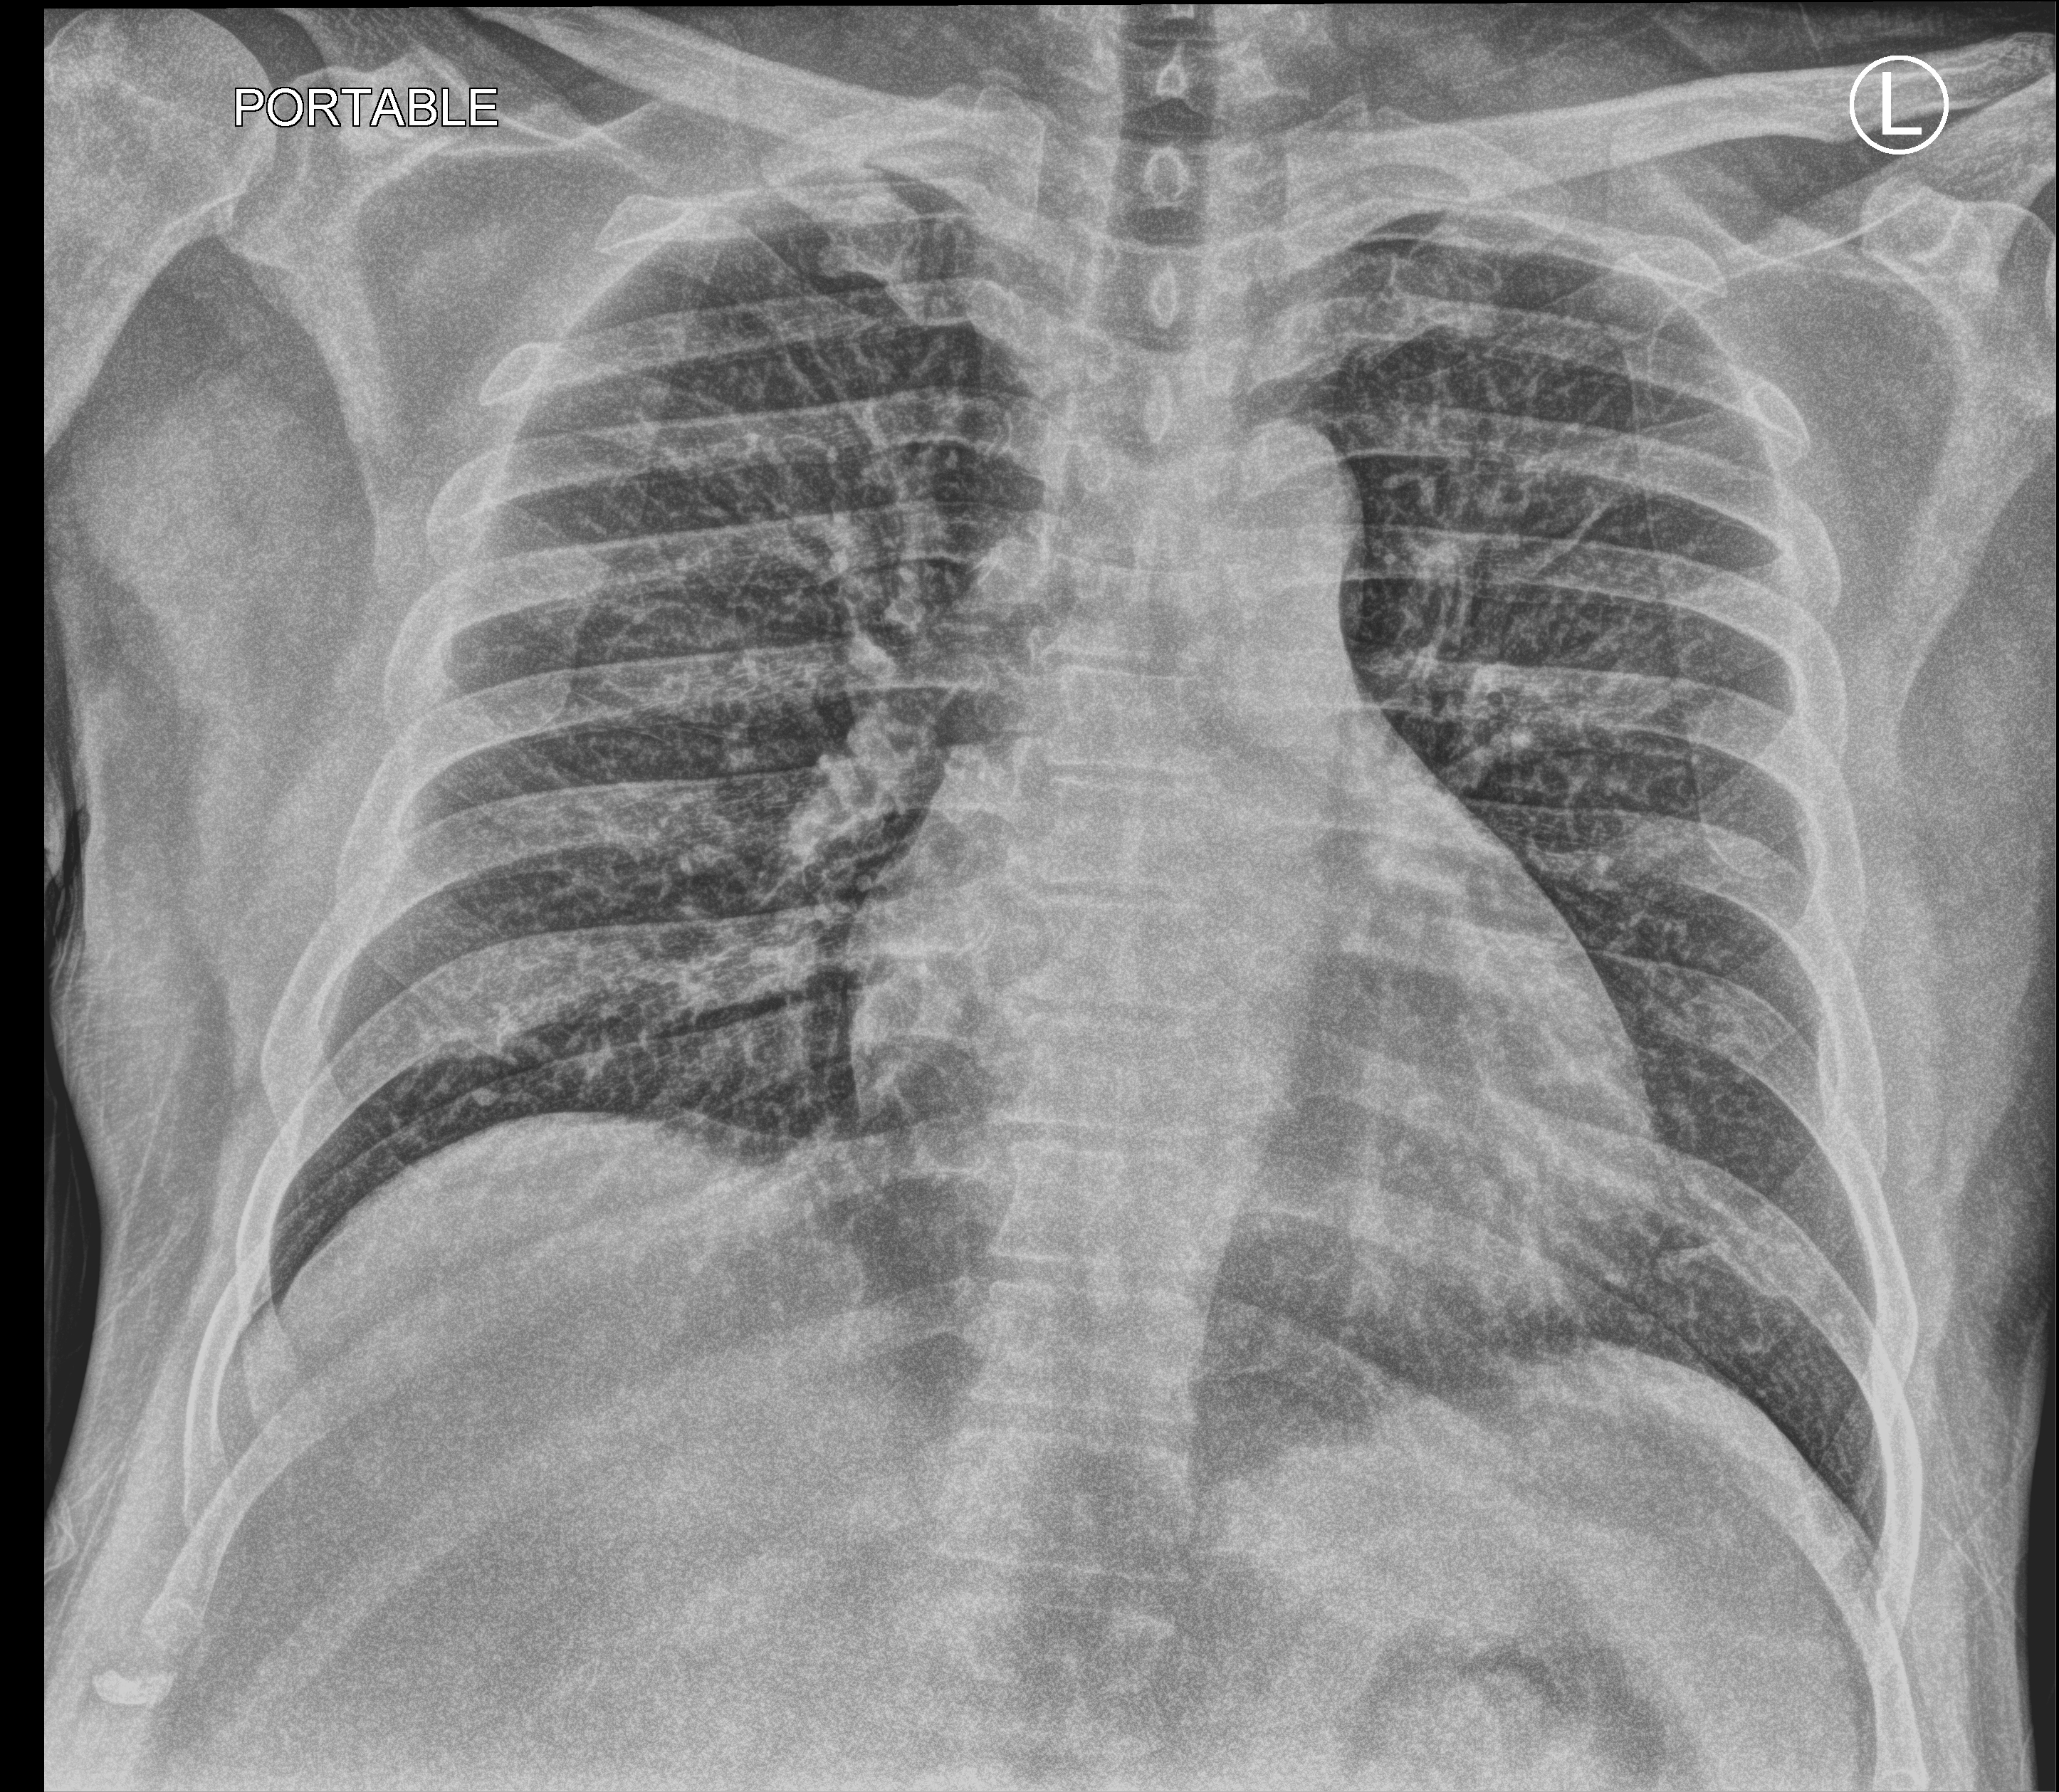
Portable chest radiograph; anteroposterior (AP) projection. Patient hospitalised with COVID-19; male, aged 18–59 years.
Admission-level facts for this patient (not findings on this image; timing relative to this image not recorded): length of hospital stay: 3 days; admitted to intensive care during this hospital stay: no; mechanically ventilated during this hospital stay: no.